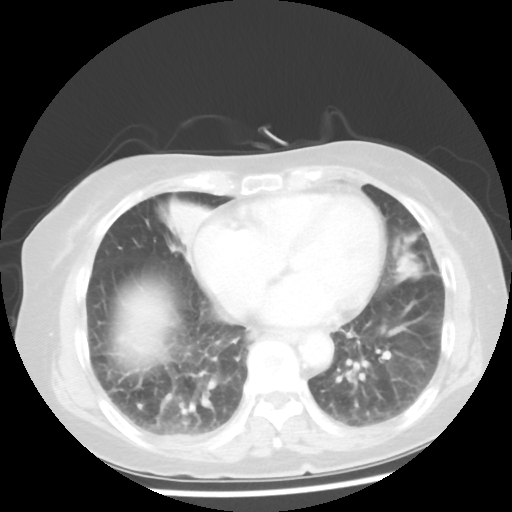
Chest CT, one axial slice; position 16 of 50 along the scan axis; reconstruction kernel STANDARD; lung window (W 1500 / L -600 HU); 512 × 512 image matrix. Patient: female, 77 years. From the clinical record (not read from this slice): clinical TNM (as recorded): T2 N3 M1a.
Structures marked on this image (rectangle marked by the reading radiologist):
- lung tumour (recorded histology: adenocarcinoma): bounding box <391,229,424,284> (left, top, right, bottom; pixels)